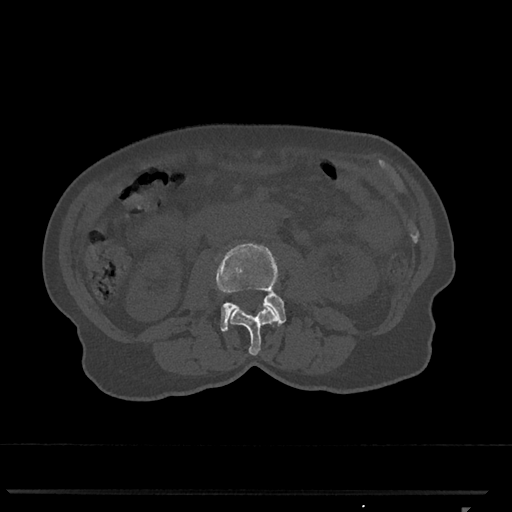
CT including the spine, one axial slice. Position 301 of 793 along the scan axis. Reconstruction kernel Br40s/3. Bone window (W 1800 / L 400 HU). 0.5 mm slice thickness. 512 × 512 image matrix, field of view 380 × 380 mm. Patient: female, 62 years. From the clinical record (not read from this slice): primary cancer: renal.
Annotated regions visible in this slice (semi-automatically segmented with operator editing):
- L2 vertebra: bounding box [x1, y1, x2, y2] px = [229, 305, 278, 356]
- L3 vertebra: [217, 243, 286, 332]